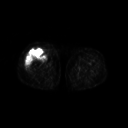
FDG PET of an extremity soft-tissue mass (from a PET/CT study), one axial slice. Slice 232 of 311 in the series (ordered by position). 3.27 mm slice thickness. 128 × 128 image matrix, field of view 500 × 500 mm. Female patient, age 57 years. From the clinical record (not read from this slice): histological type: pleiomorphic undifferentiated sarcoma; grade: high; site of the primary tumour: right quadricep.
Structures marked on this image (expert contour drawn on MRI and transferred to this co-registered scan by the dataset authors):
- tumour plus oedema (research contour): box from (x=25, y=50) to (x=46, y=70) px
- tumour (research contour): (x=25, y=50)–(x=46, y=70)